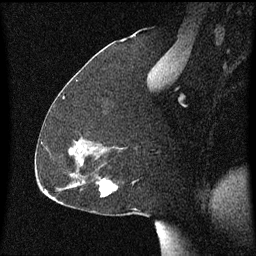
Breast MRI (dynamic contrast-enhanced), one sagittal slice. Position 33 of 60 along the scan axis. Dynamic contrast-enhanced series, image 2 of 3 at this slice position (ordered by acquisition). 1.5 T. TE 4.2 ms, TR 8.4 ms. 256 × 256 image matrix, field of view 200 × 200 mm. Patient: female, 59 years.
Outlined on this slice (semi-automatically segmented with operator editing):
- analysis volume of interest (the breast-tissue region the enhancement analysis was run in; not a lesion): bounding box <96,176,135,197> (left, top, right, bottom; pixels)
- tumour enhancement mask (voxels above the 70 % enhancement threshold inside the analysis volume of interest): <102,180,117,197>